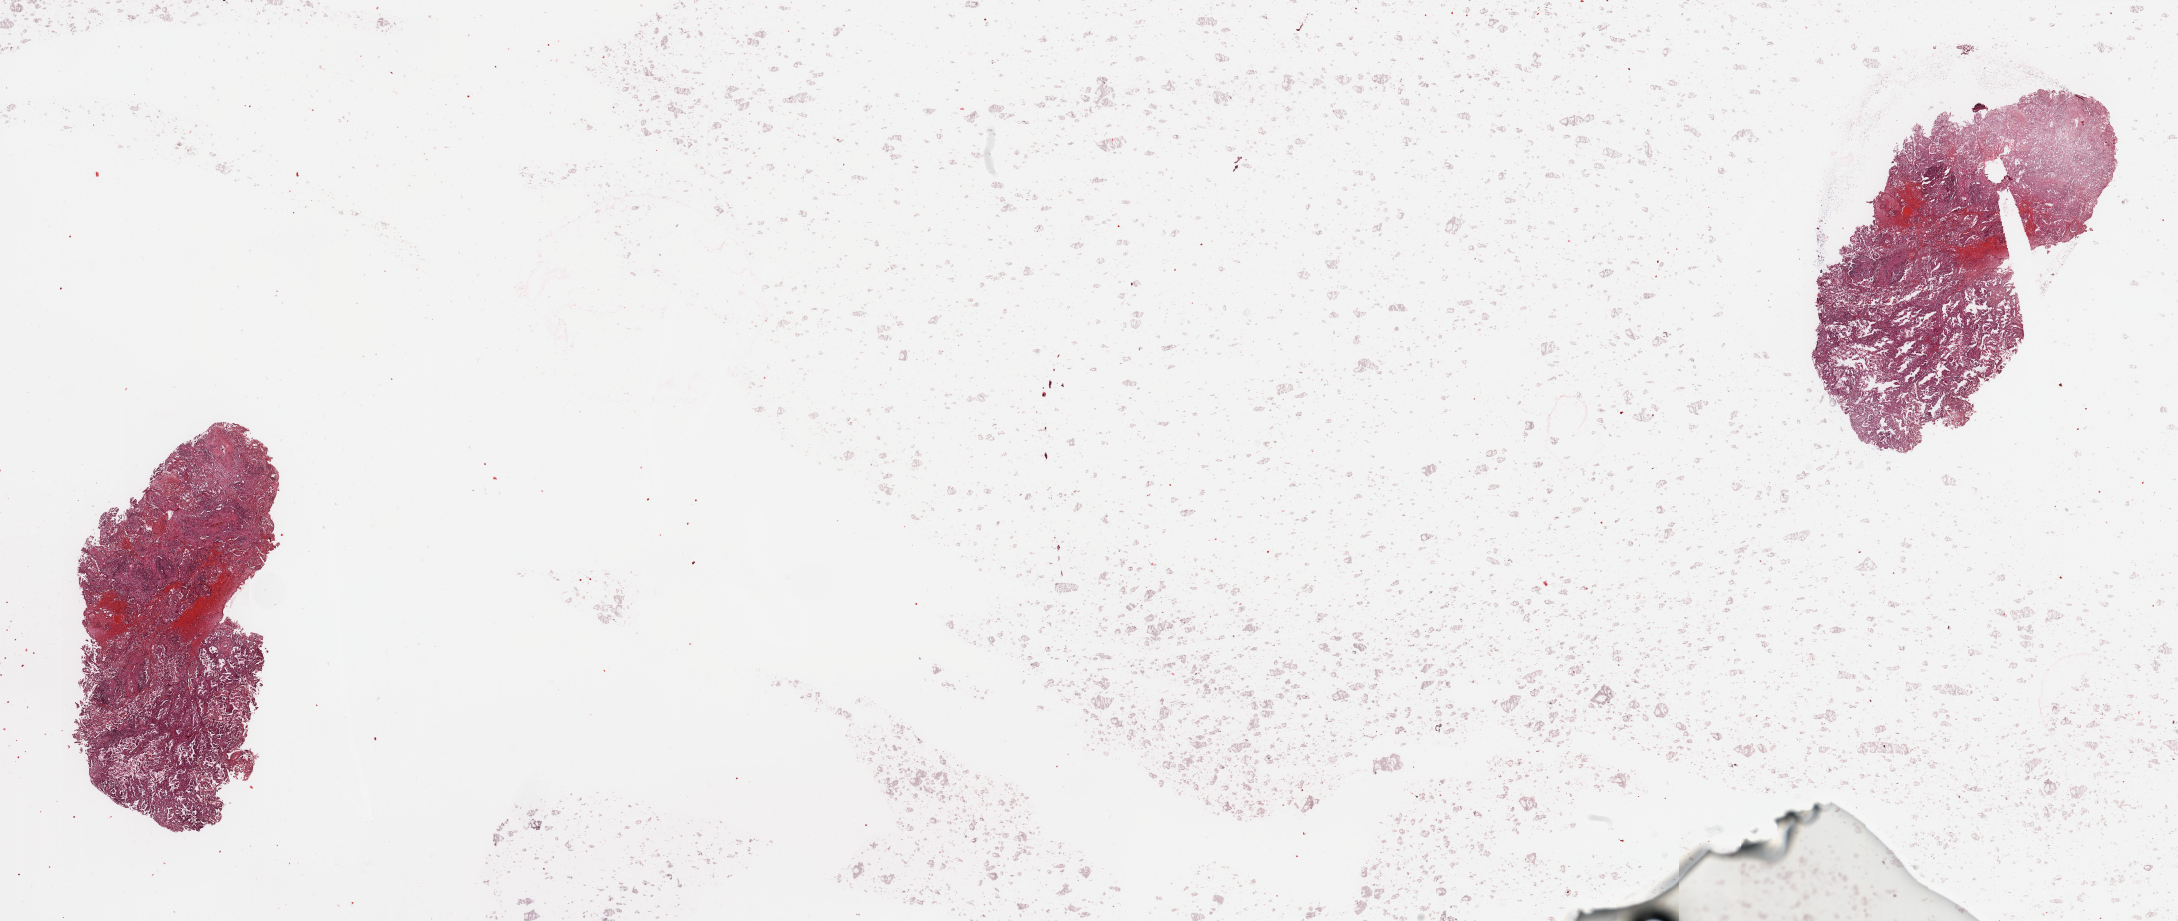
Digitized Hematoxylin and eosin (H&E) stained tissue section (whole slide), whole scanned area (about 34.5 x 14.6 mm) shown as a low-resolution overview; lung, tumour tissue. 59-year-old male patient. Histologic grade: G2 (moderately differentiated).
* diagnosis: Adenocarcinoma, NOS
* AJCC pathologic stage: IIIA